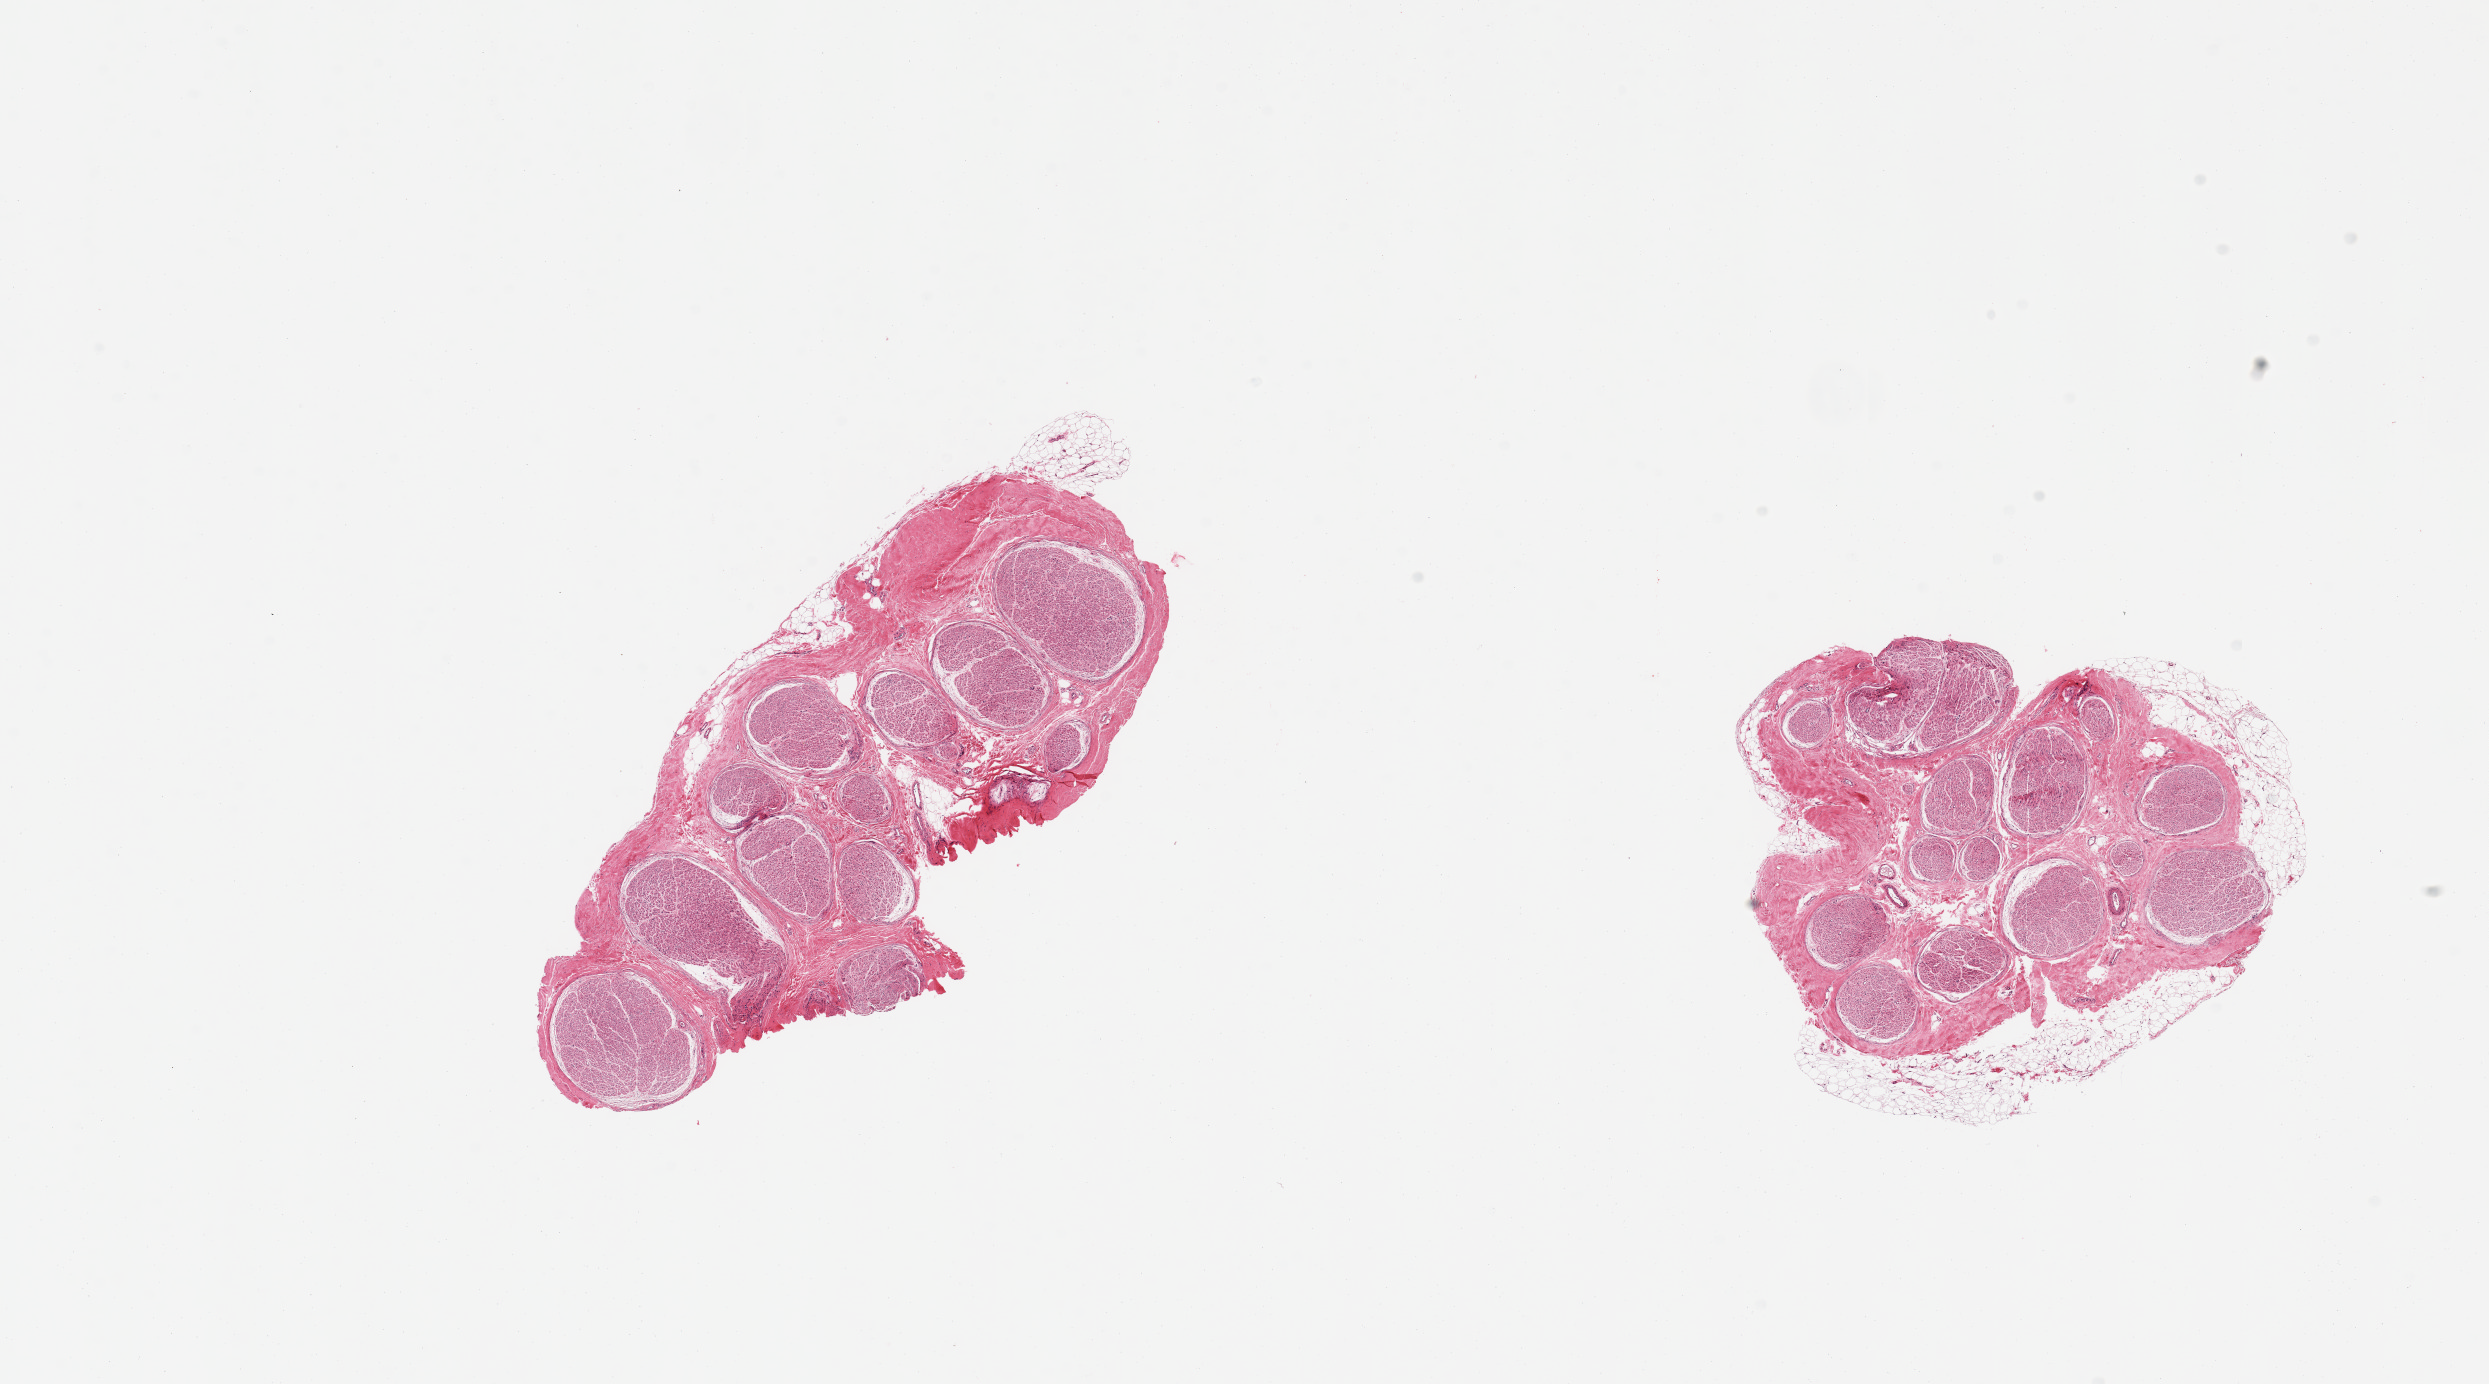
Digitized H&E-stained section, brightfield — a low-resolution overview of the entire scanned area, about 19.7 x 10.9 mm. PAXgene-fixed paraffin-embedded (PFPE) section. Section of tibial nerve (target tissue). Donor tissue sample. Donor sex: male.
Reviewer comment on this tissue sample: 2 pieces; 0.8mm and 1.0 mm of attached external fat and connective tissue.